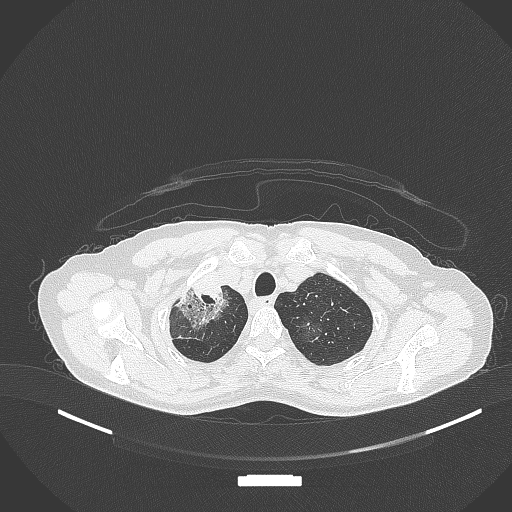
Chest CT, one axial slice; 120 kVp; lung window (W 1500 / L -600 HU); 1 mm slice thickness; 512 × 512 image matrix, field of view 400 × 400 mm. Patient: female, 59 years. From the clinical record (not read from this slice): clinical TNM (as recorded): T3 N0 M0; histopathological grade: G1.
Annotated regions visible in this slice (rectangle marked by the reading radiologist):
- lung tumour (recorded histology: adenocarcinoma): box from (x=173, y=281) to (x=223, y=330) px